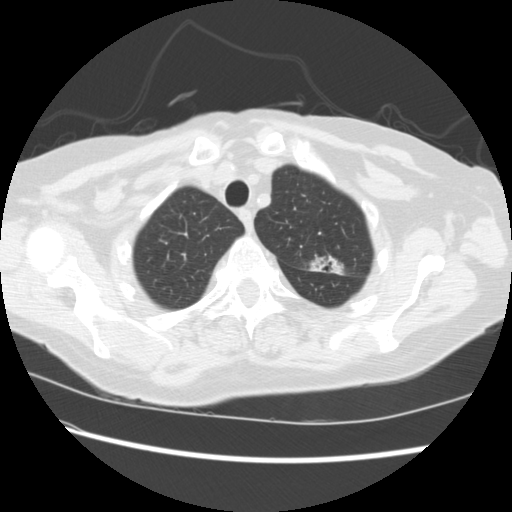
Low-dose screening chest CT, one axial slice; slice 186 of 224 in the series (ordered by position); lung window (W 1500 / L -600 HU); 2.5 mm slice thickness; 512 × 512 image matrix, field of view 340 × 340 mm.
Annotated regions visible in this slice (expert manual segmentation):
- lesion 1 (tumor, upper lobe of left lung): bounding box <310,257,344,275> (left, top, right, bottom; pixels)